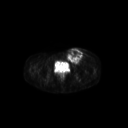
FDG PET of an extremity soft-tissue mass (from a PET/CT study), one axial slice; position 67 of 267 along the scan axis; 3.27 mm slice thickness; 128 × 128 image matrix, field of view 600 × 600 mm. Female patient, age 24 years. Case-level facts recorded for this patient, not image findings: histological type: leiomyosarcoma; grade: high; site of the primary tumour: groin.
Structures marked on this image (expert contour drawn on MRI and transferred to this co-registered scan by the dataset authors):
- gross tumour volume including surrounding oedema: bounding box [x1, y1, x2, y2] px = [66, 48, 90, 64]
- gross tumour volume (mass): [66, 48, 84, 64]